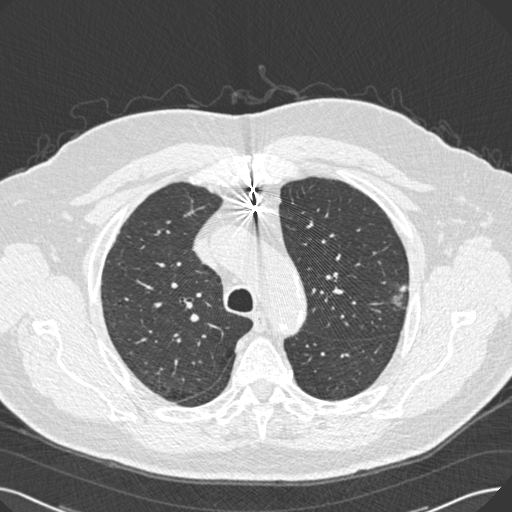
Low-dose screening chest CT, one axial slice. Slice 198 of 269 in the series (ordered by position). Reconstruction kernel B30f. Lung window (W 1500 / L -600 HU). 1 mm slice thickness. 512 × 512 image matrix, field of view 370 × 370 mm.
Outlined on this slice (outlined manually by an expert reader):
- lesion 1 (tumor, upper lobe of left lung): box from (x=394, y=285) to (x=409, y=306) px